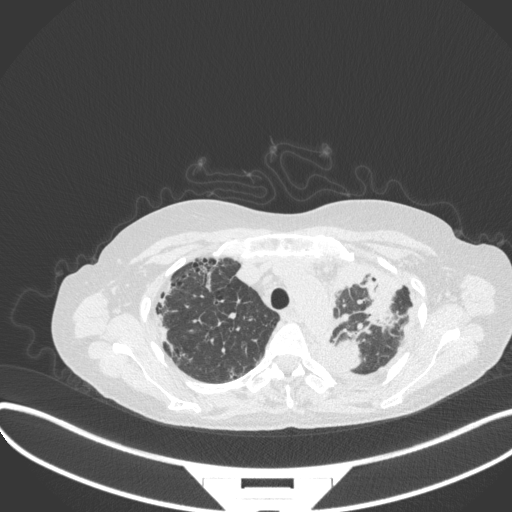
Chest CT, one axial slice. Reconstruction kernel B31f. Lung window (W 1500 / L -600 HU). 1 mm slice thickness. 512 × 512 image matrix, field of view 400 × 400 mm. Patient: female, 56 years. Case-level facts recorded for this patient, not image findings: clinical TNM (as recorded): T1 N0 M0.
Structures marked on this image (bounding box drawn by a radiologist):
- lung tumour (recorded histology: adenocarcinoma): bounding box (x1, y1, x2, y2) in pixels: (331, 337, 365, 376)
- lung tumour (recorded histology: adenocarcinoma): (359, 264, 404, 334)